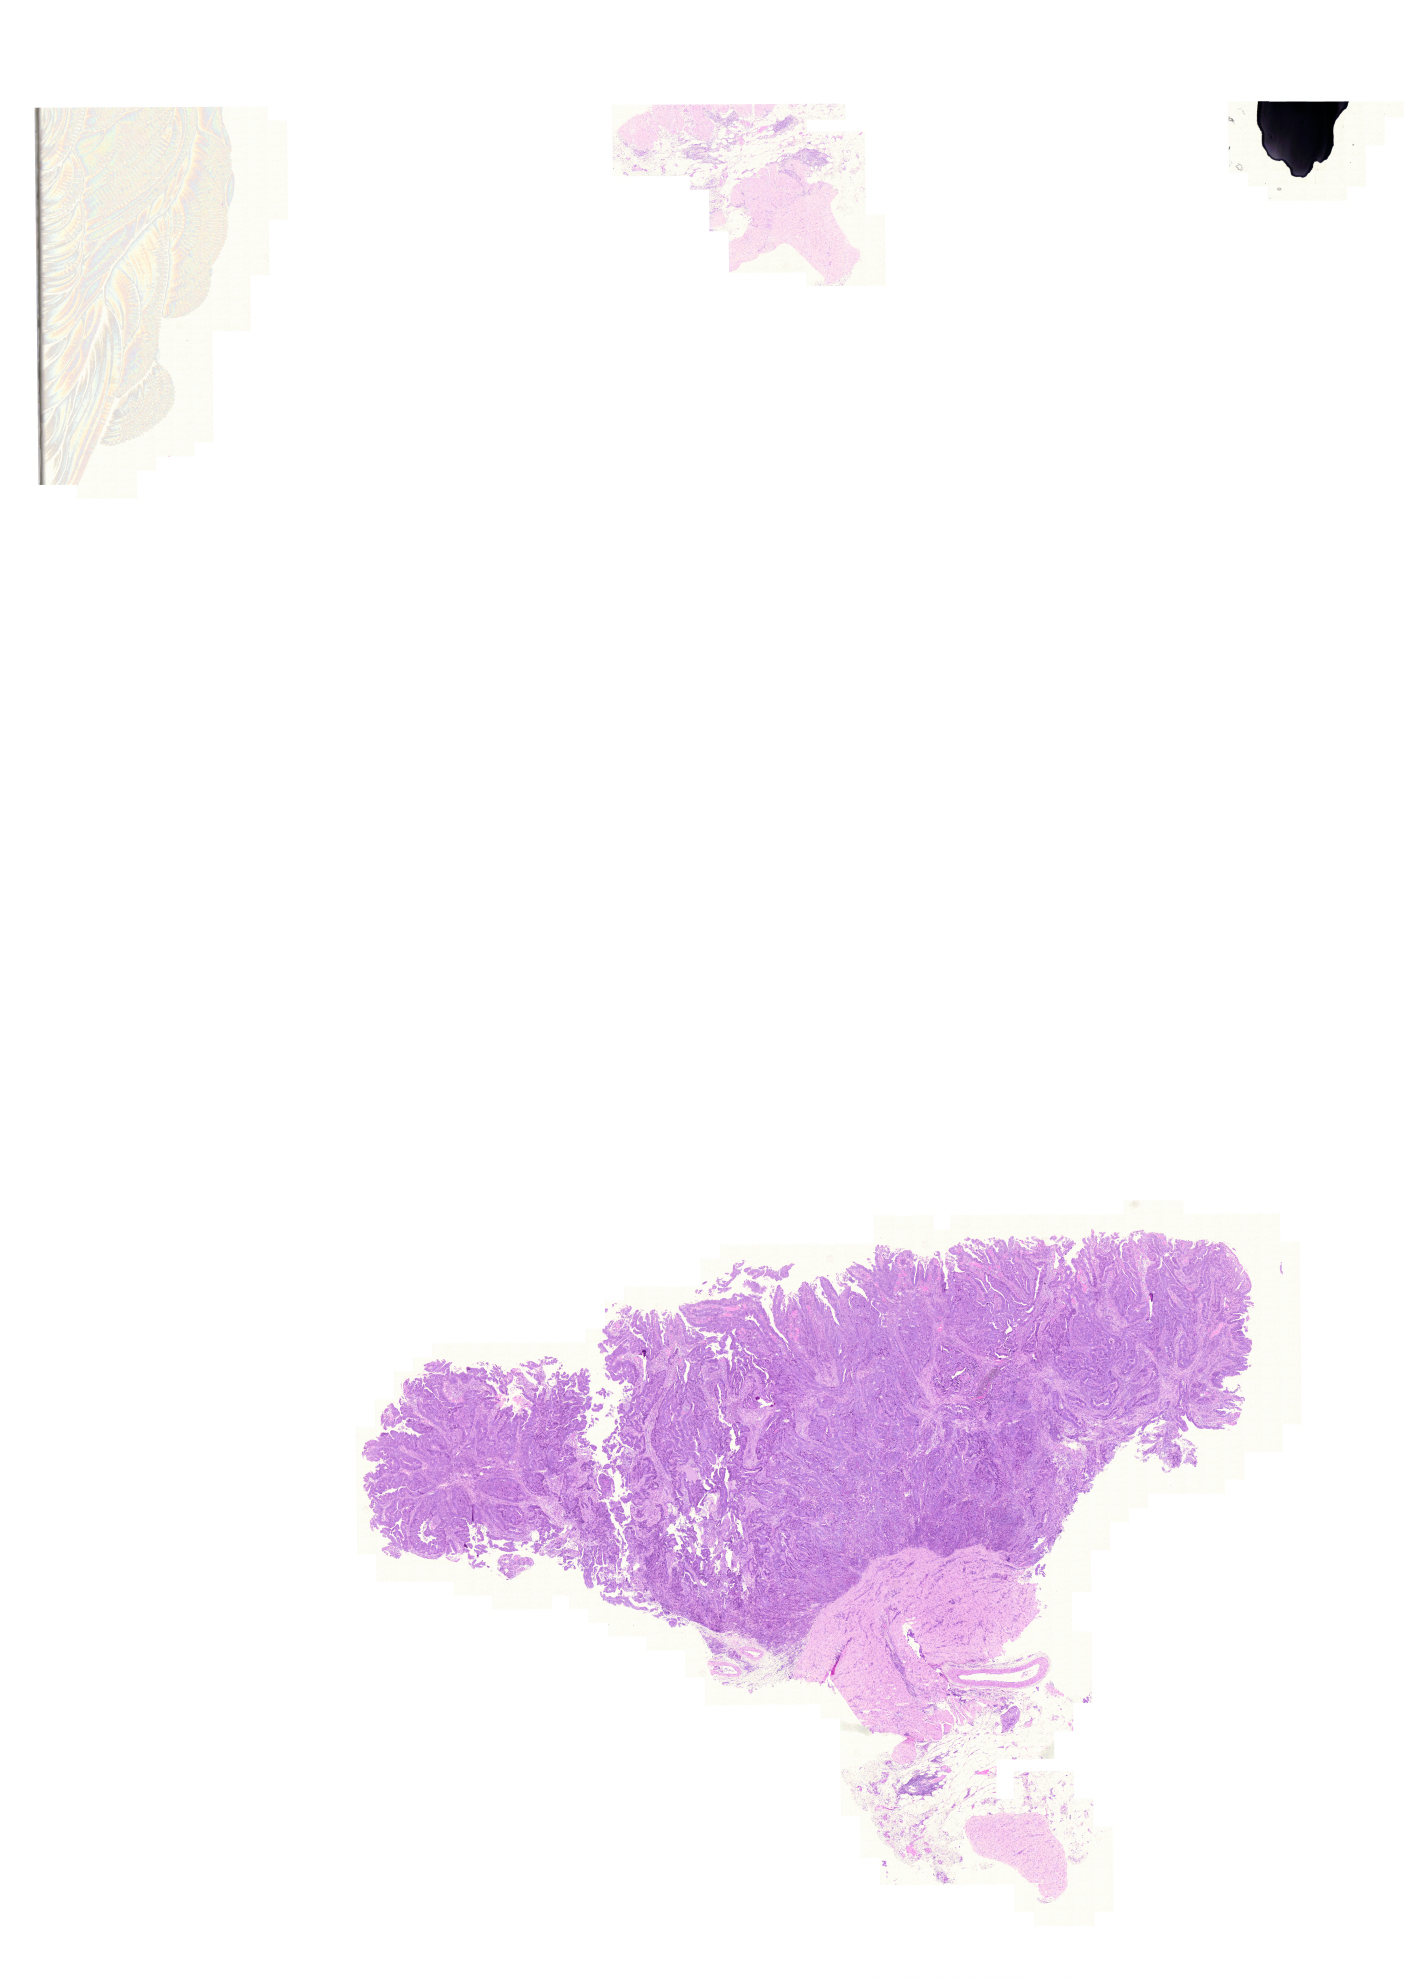
Digitized Hematoxylin and eosin (H&E) stained tissue section (whole slide) — shown as a low-resolution overview of the whole scanned area (about 21.2 x 29.5 mm). Formalin-fixed paraffin-embedded (FFPE) diagnostic section. Sample: primary tumour, rectum. Female, age 49 years at initial diagnosis.
AJCC pathologic stage: II (5th edition). Diagnosis: Adenocarcinoma, NOS.